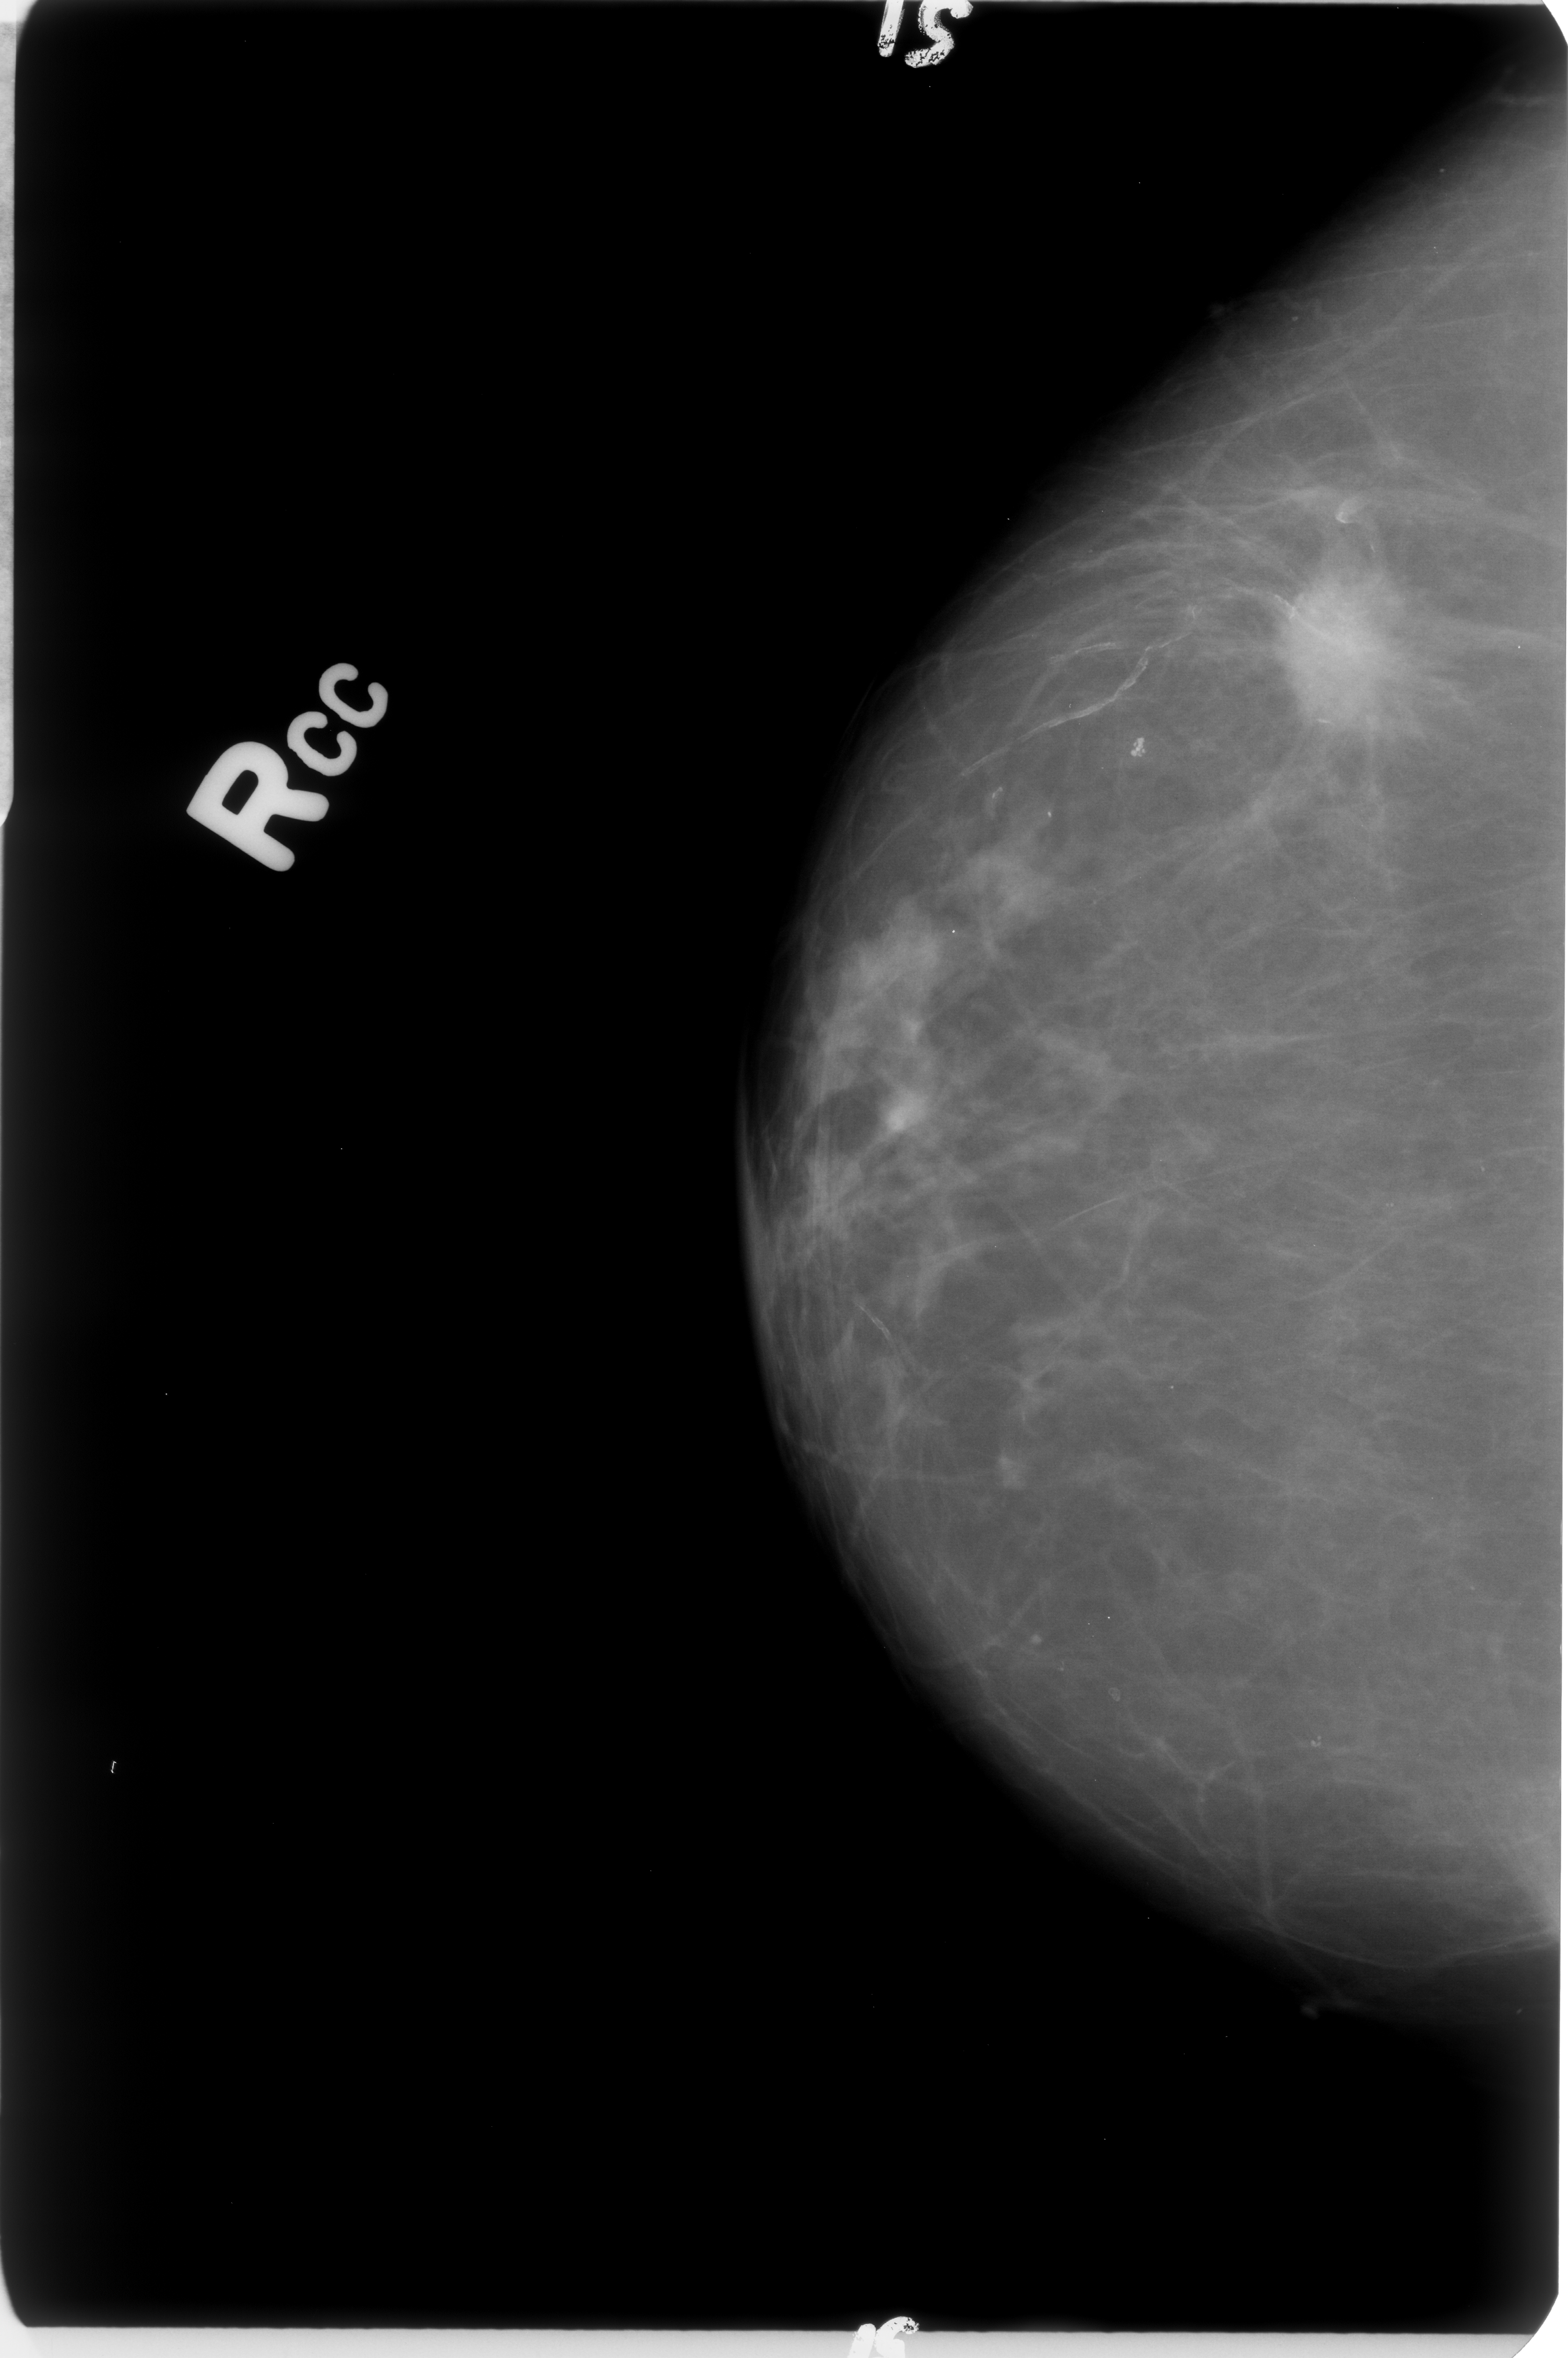
Mammogram (digitized film). Right breast. CC view. Breast composition: scattered fibroglandular densities (BI-RADS density category 2 of 4). 1568 × 2358 image matrix.
Expert-marked regions of interest on this image (one box per marked abnormality):
- mass, shape irregular / architectural distortion, margins spiculated; BI-RADS assessment category 5; subtlety rating 5 on a 1 (subtle) to 5 (obvious) scale; pathology result (as recorded, not read from the image): malignant: bounding box <1257,556,1415,731> (left, top, right, bottom; pixels)